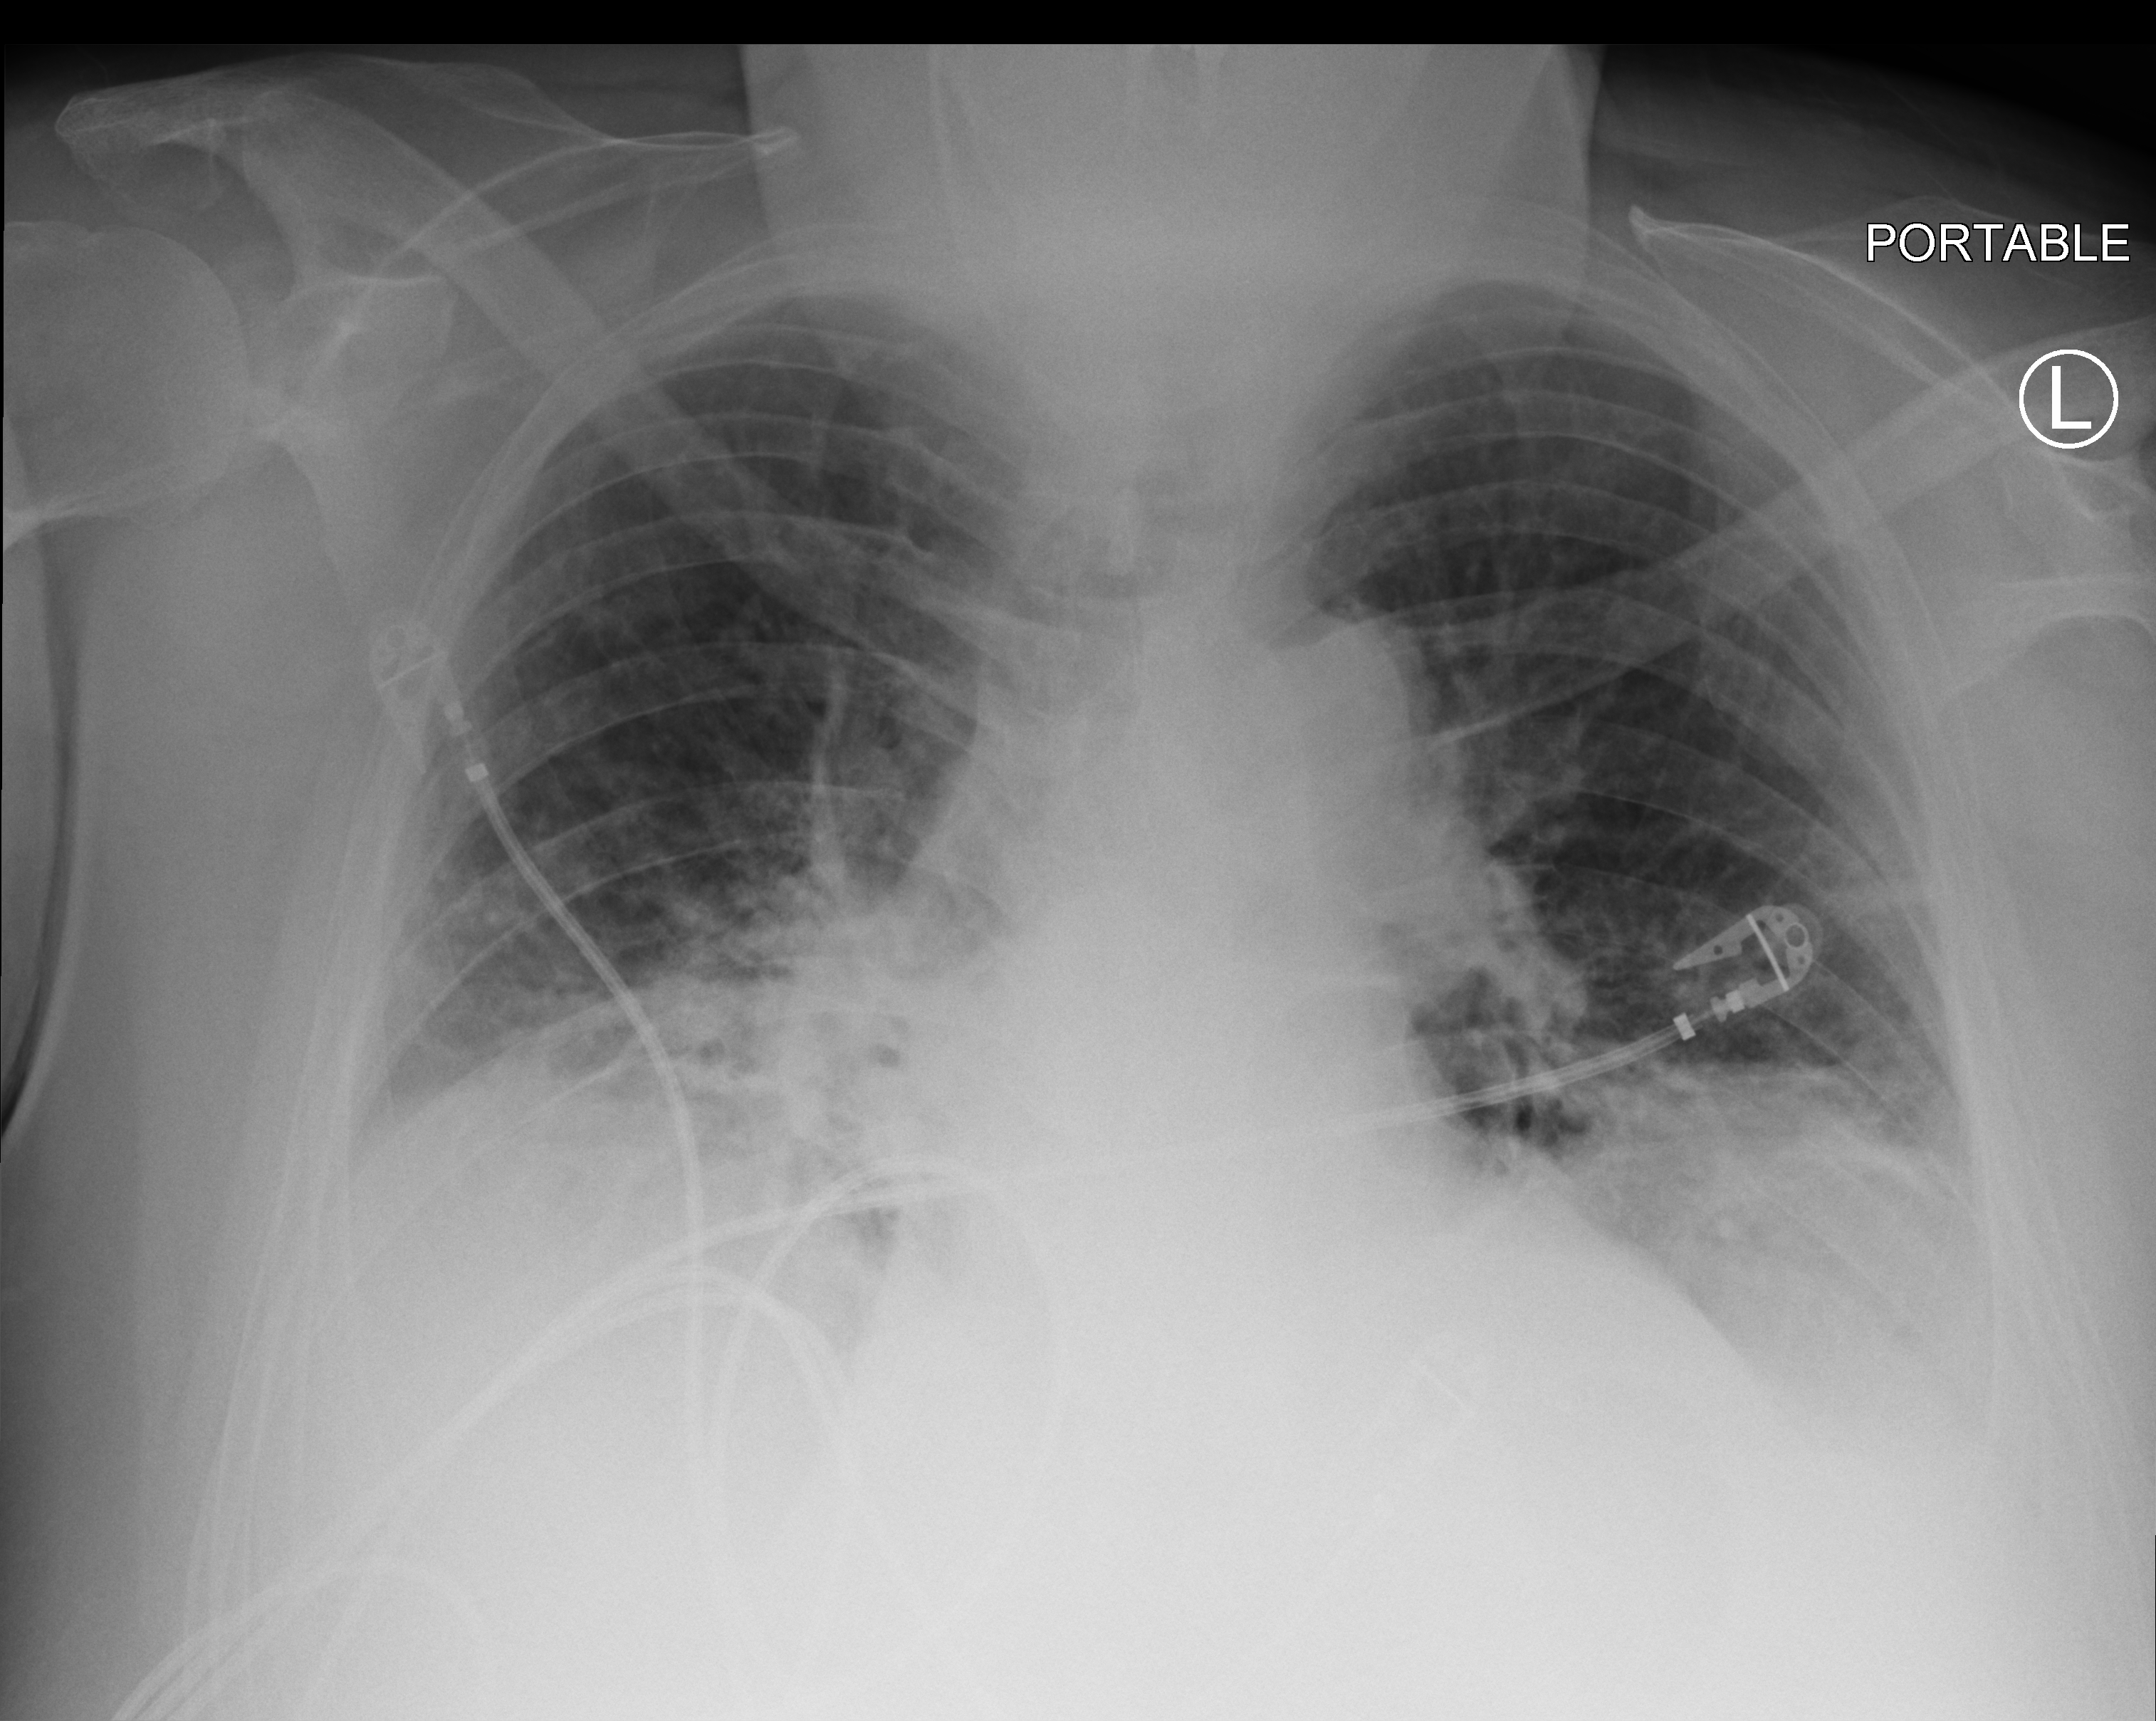
Portable chest radiograph; anteroposterior (AP) projection. Patient hospitalised with COVID-19; male, aged 60–74 years.
Admission-level facts for this patient (not findings on this image; timing relative to this image not recorded): mechanically ventilated during this hospital stay: yes.